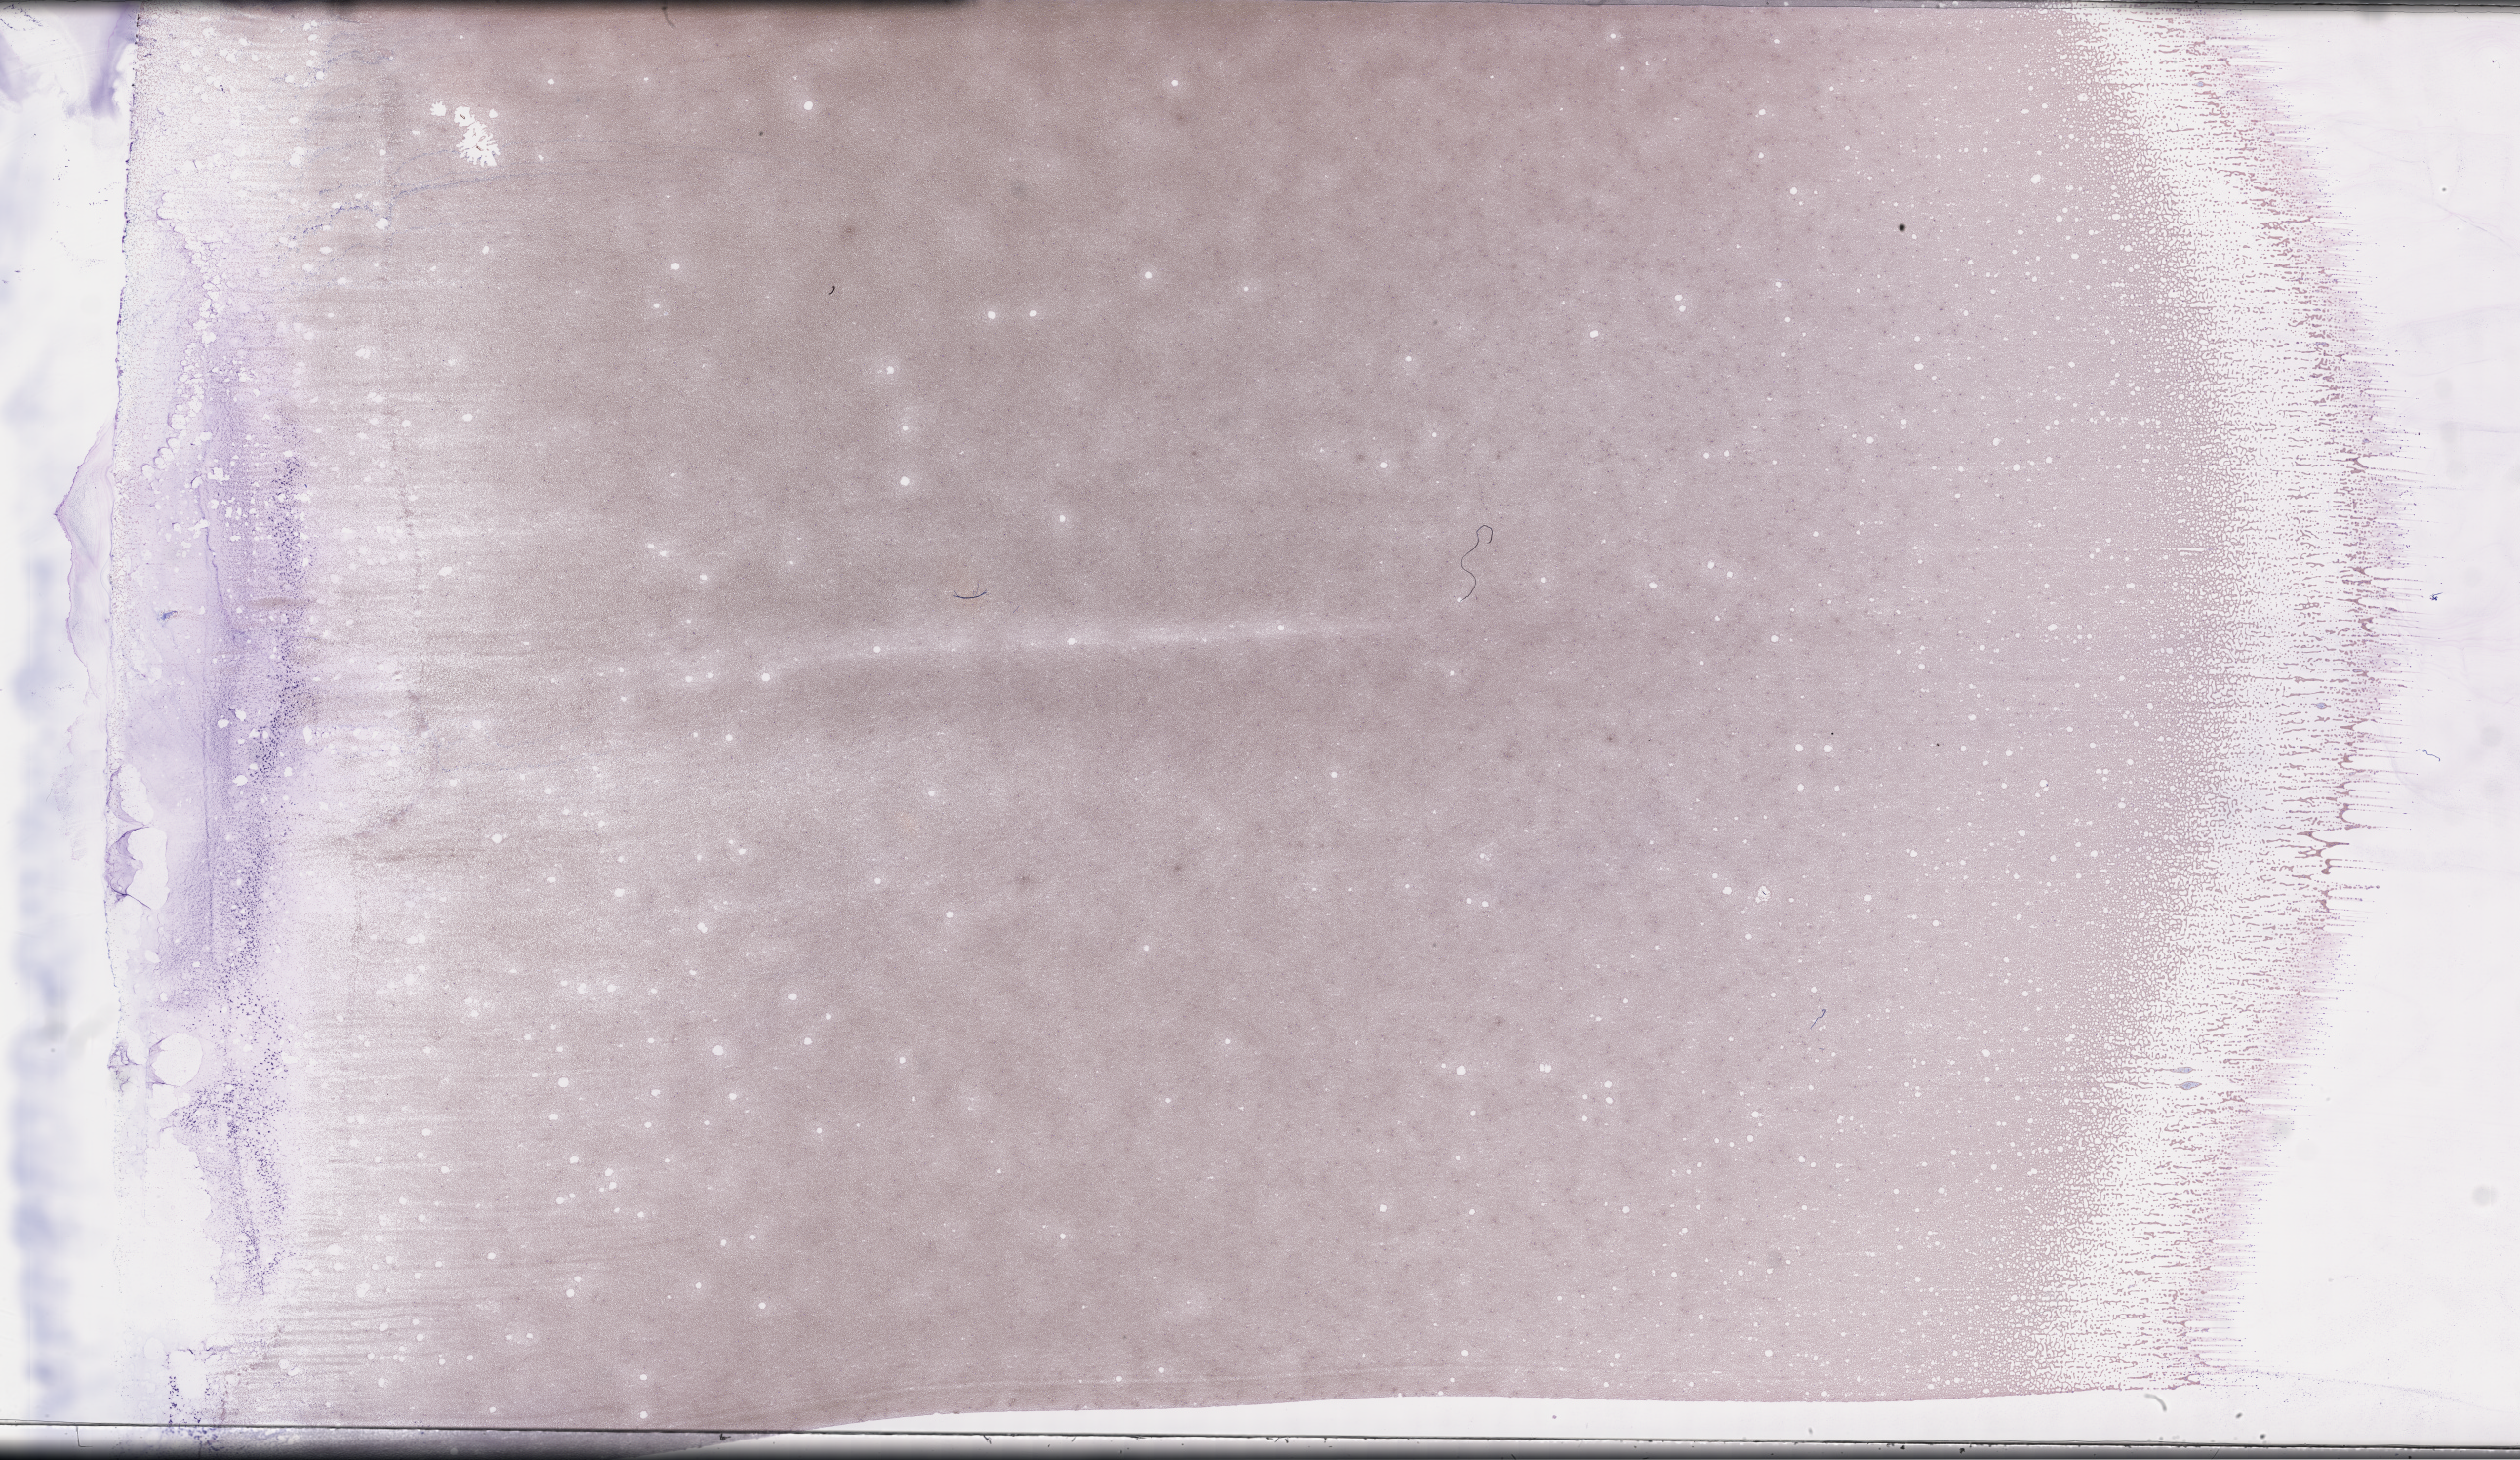
Whole-slide image of a whole blood smear, Wright-Giemsa stain — whole scanned area (about 41.7 x 24.2 mm) shown as a low-resolution overview; collected on treatment. Female patient.
From a patient with: Plasma Cell Myeloma.